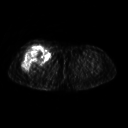
FDG PET of an extremity soft-tissue mass (from a PET/CT study), one axial slice; position 255 of 311 along the scan axis; 3.27 mm slice thickness; 128 × 128 image matrix, field of view 500 × 500 mm. Patient: female, 57 years. Case-level facts recorded for this patient, not image findings: histological type: pleiomorphic undifferentiated sarcoma; grade: high; site of the primary tumour: right quadricep.
Outlined on this slice (expert contour drawn on MRI and transferred to this co-registered scan by the dataset authors):
- tumour plus oedema (research contour): bounding box [x1, y1, x2, y2] px = [22, 45, 50, 73]
- tumour (research contour): [22, 45, 50, 73]